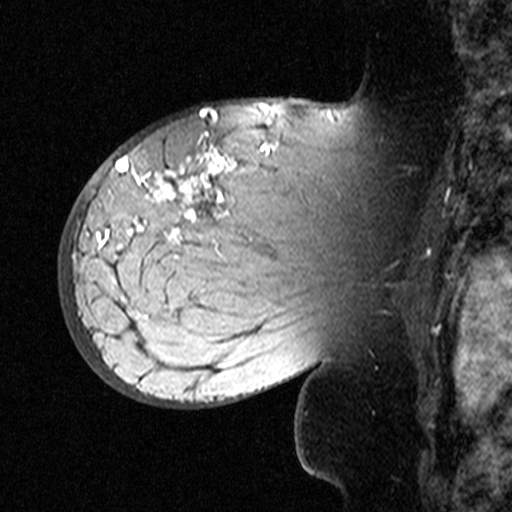
Breast MRI (dynamic contrast-enhanced), one sagittal slice; position 30 of 44 along the scan axis; dynamic contrast-enhanced study with each time point stored as its own series, time point 2 of 3 at this slice position (early post-contrast, ordered by acquisition time); 1.5 T; TE 4.5 ms, TR 11 ms; 3 mm slice thickness; 512 × 512 image matrix. Female patient, age 53 years. Case-level facts recorded for this patient, not image findings: setting: breast cancer imaged before/during neoadjuvant chemotherapy; receptor status: HR-positive, HER2-negative.
Annotated regions visible in this slice (semi-automatically segmented with operator editing):
- analysis volume of interest (the breast-tissue region the enhancement analysis was run in; not a lesion): bounding box [x1, y1, x2, y2] px = [76, 140, 311, 353]
- tumour enhancement mask (voxels above the 90 % enhancement threshold inside the analysis volume of interest): [100, 145, 268, 260]